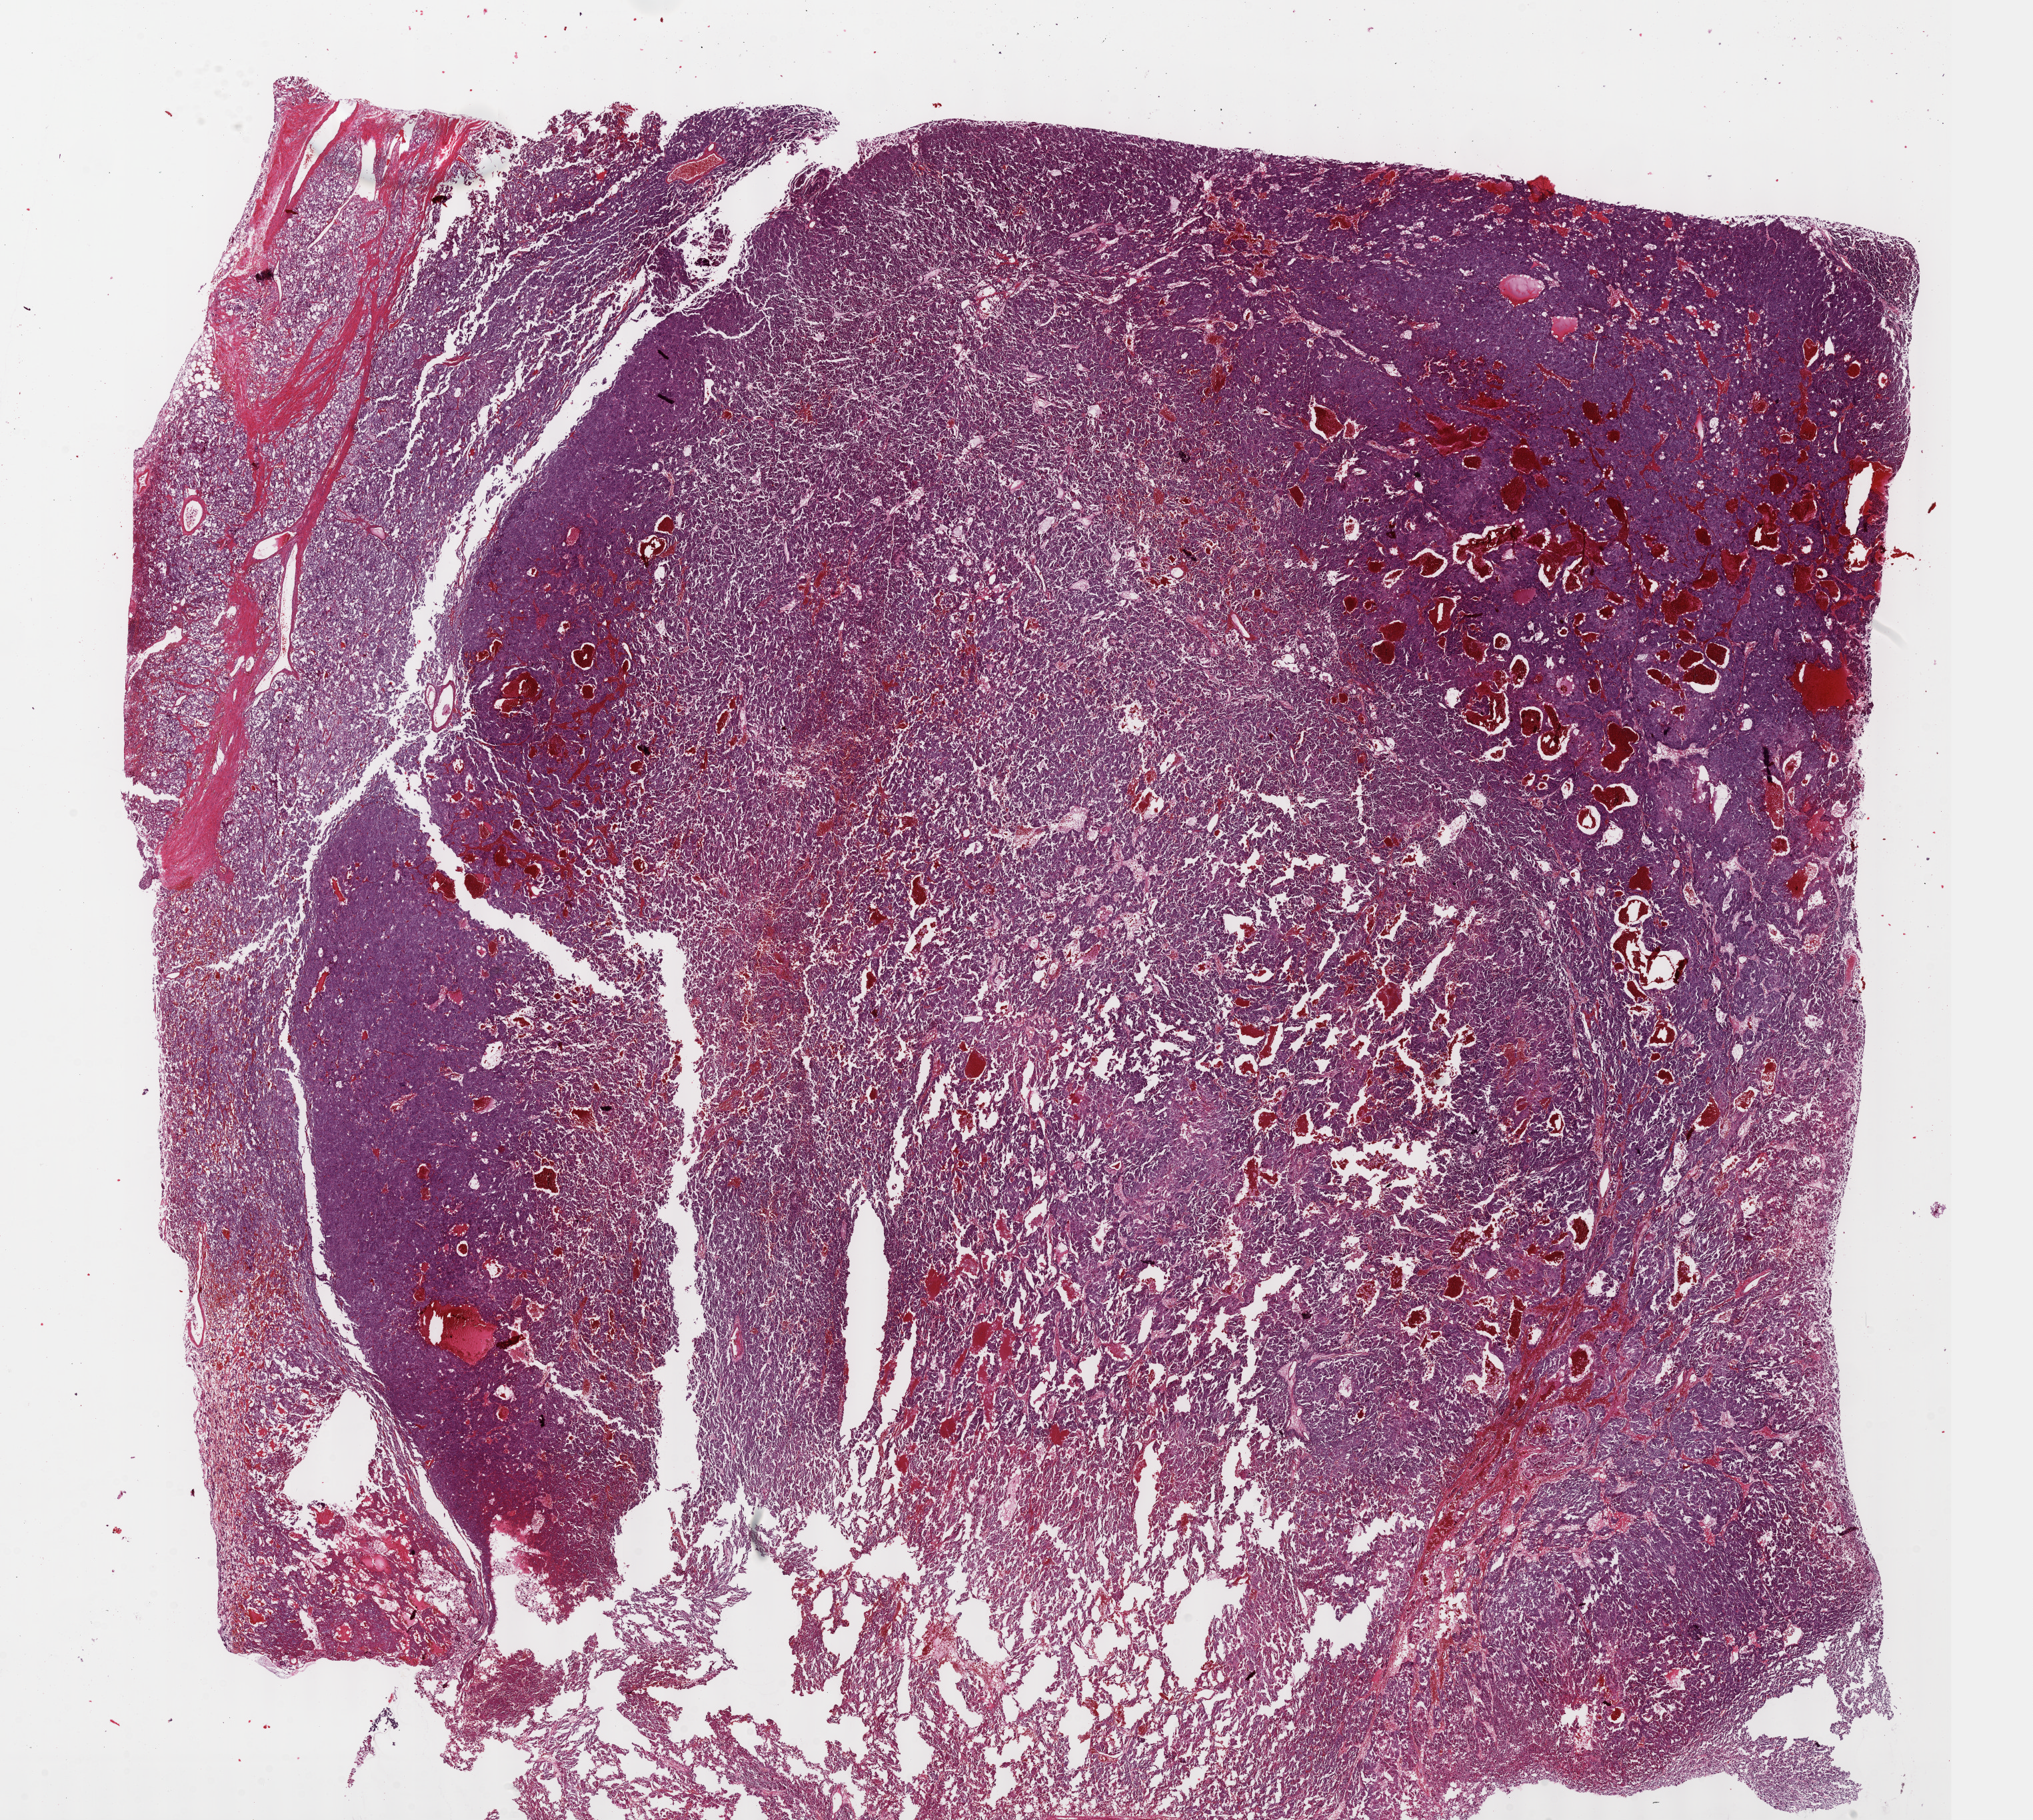
Digitized H&E-stained tissue section (whole slide) — shown as a low-resolution overview of the whole scanned area (about 24.6 x 22.1 mm, slide scanned at 40x), FFPE section, primary tumour sample from the adrenal gland. Male, age 41 years at initial diagnosis.
* diagnosis: Pheochromocytoma, NOS